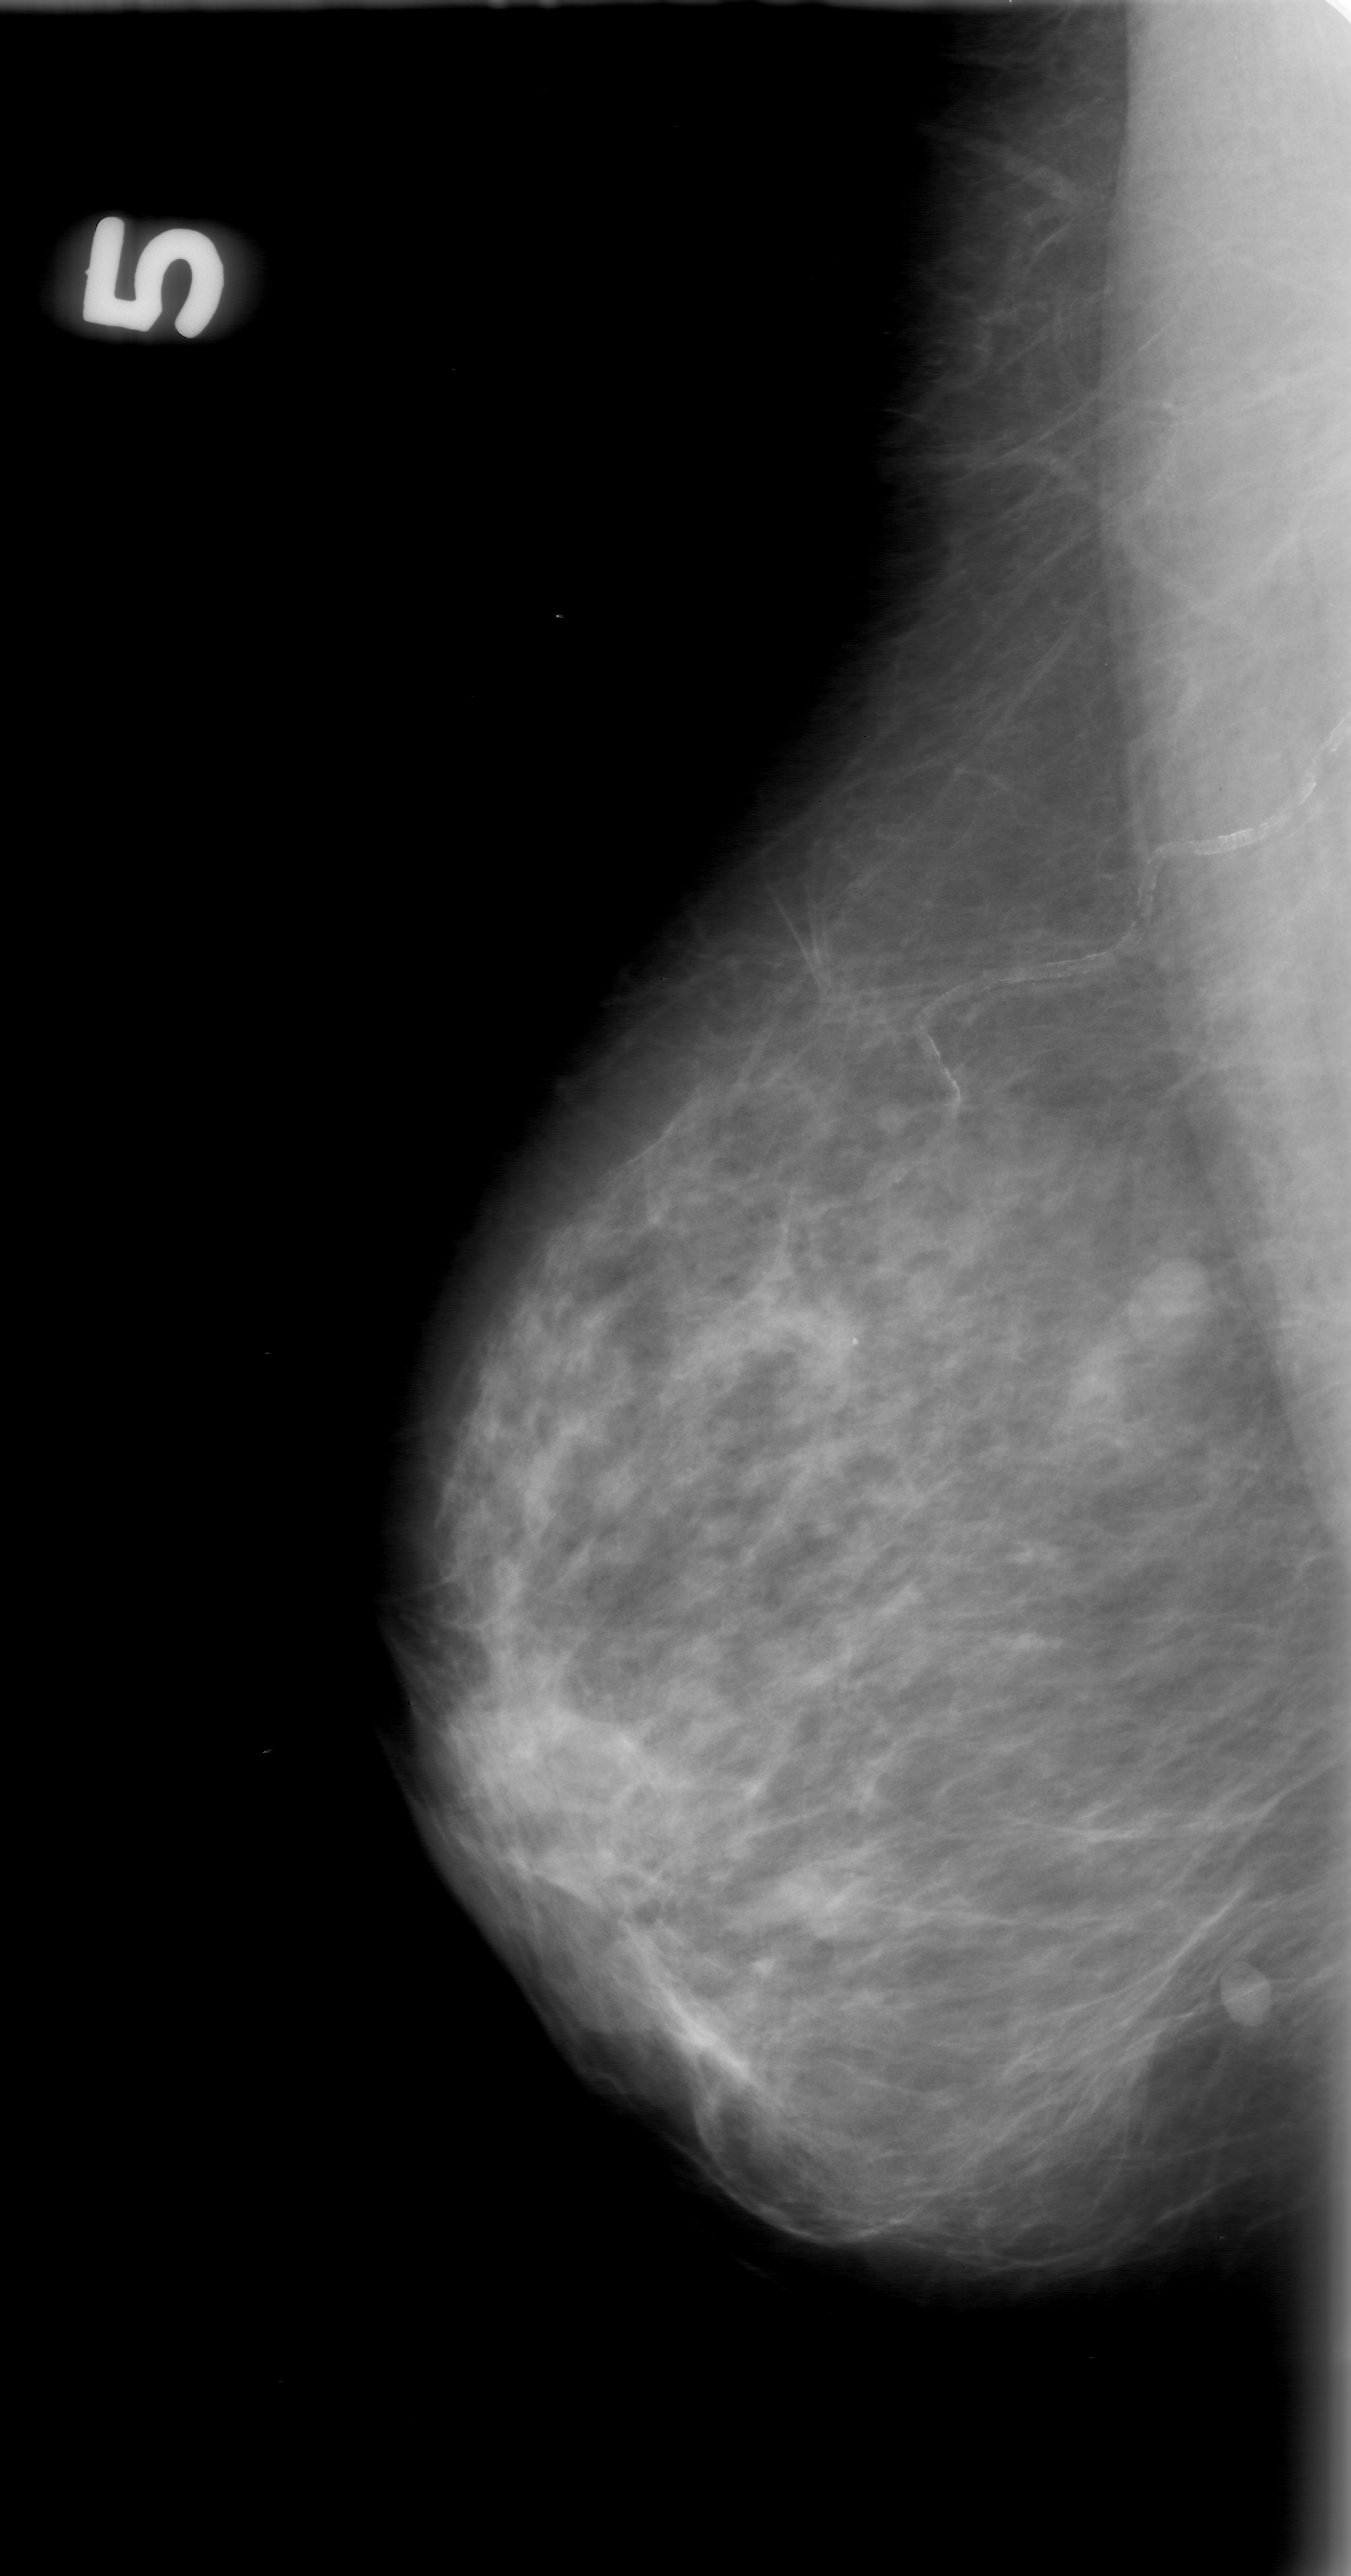
Scanned film-screen mammogram, right breast, mediolateral oblique (MLO) view, breast composition: scattered fibroglandular densities (BI-RADS density category 2 of 4).
Mass, shape oval, margins circumscribed; BI-RADS assessment category 0; subtlety rating 5 on a 1 (subtle) to 5 (obvious) scale; pathology result (as recorded, not read from the image): benign.